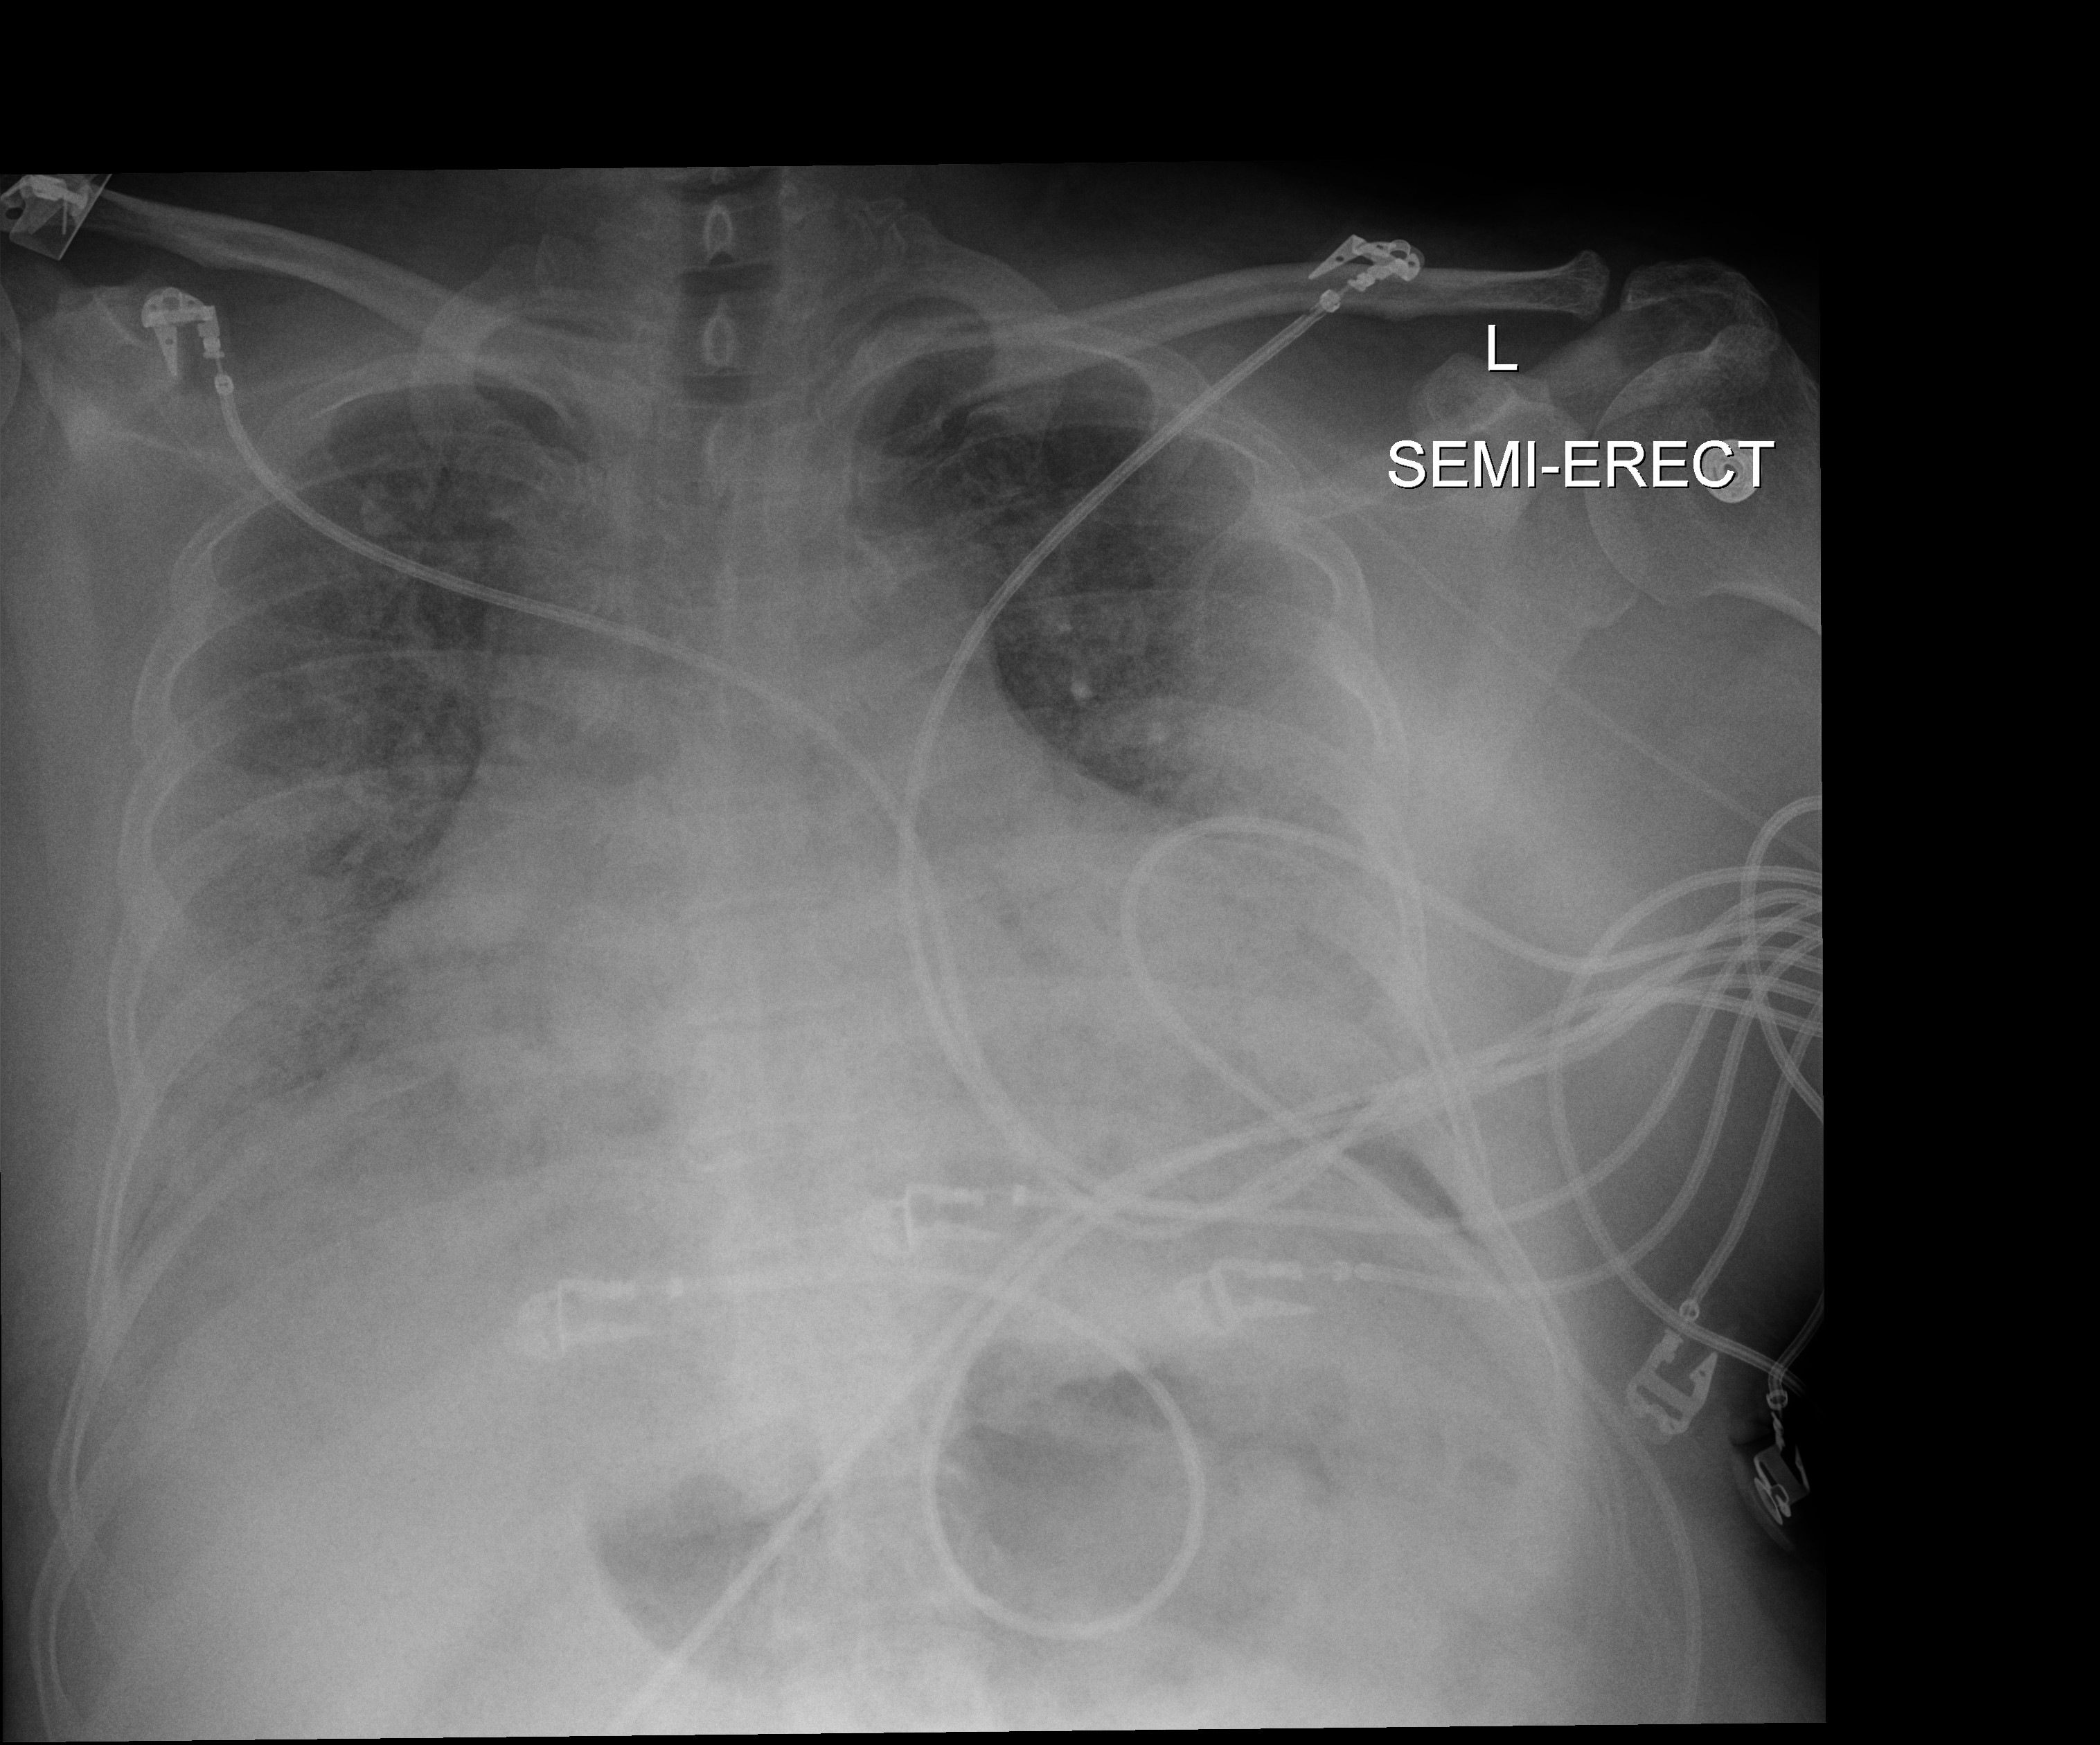
Bedside chest radiograph (digital radiography); anteroposterior (AP) projection. Adult patient hospitalised with COVID-19, age 18–59 years.
From the hospital-stay record, not from the radiograph (when in the stay this image was taken is not recorded): diabetes (admission record): no.